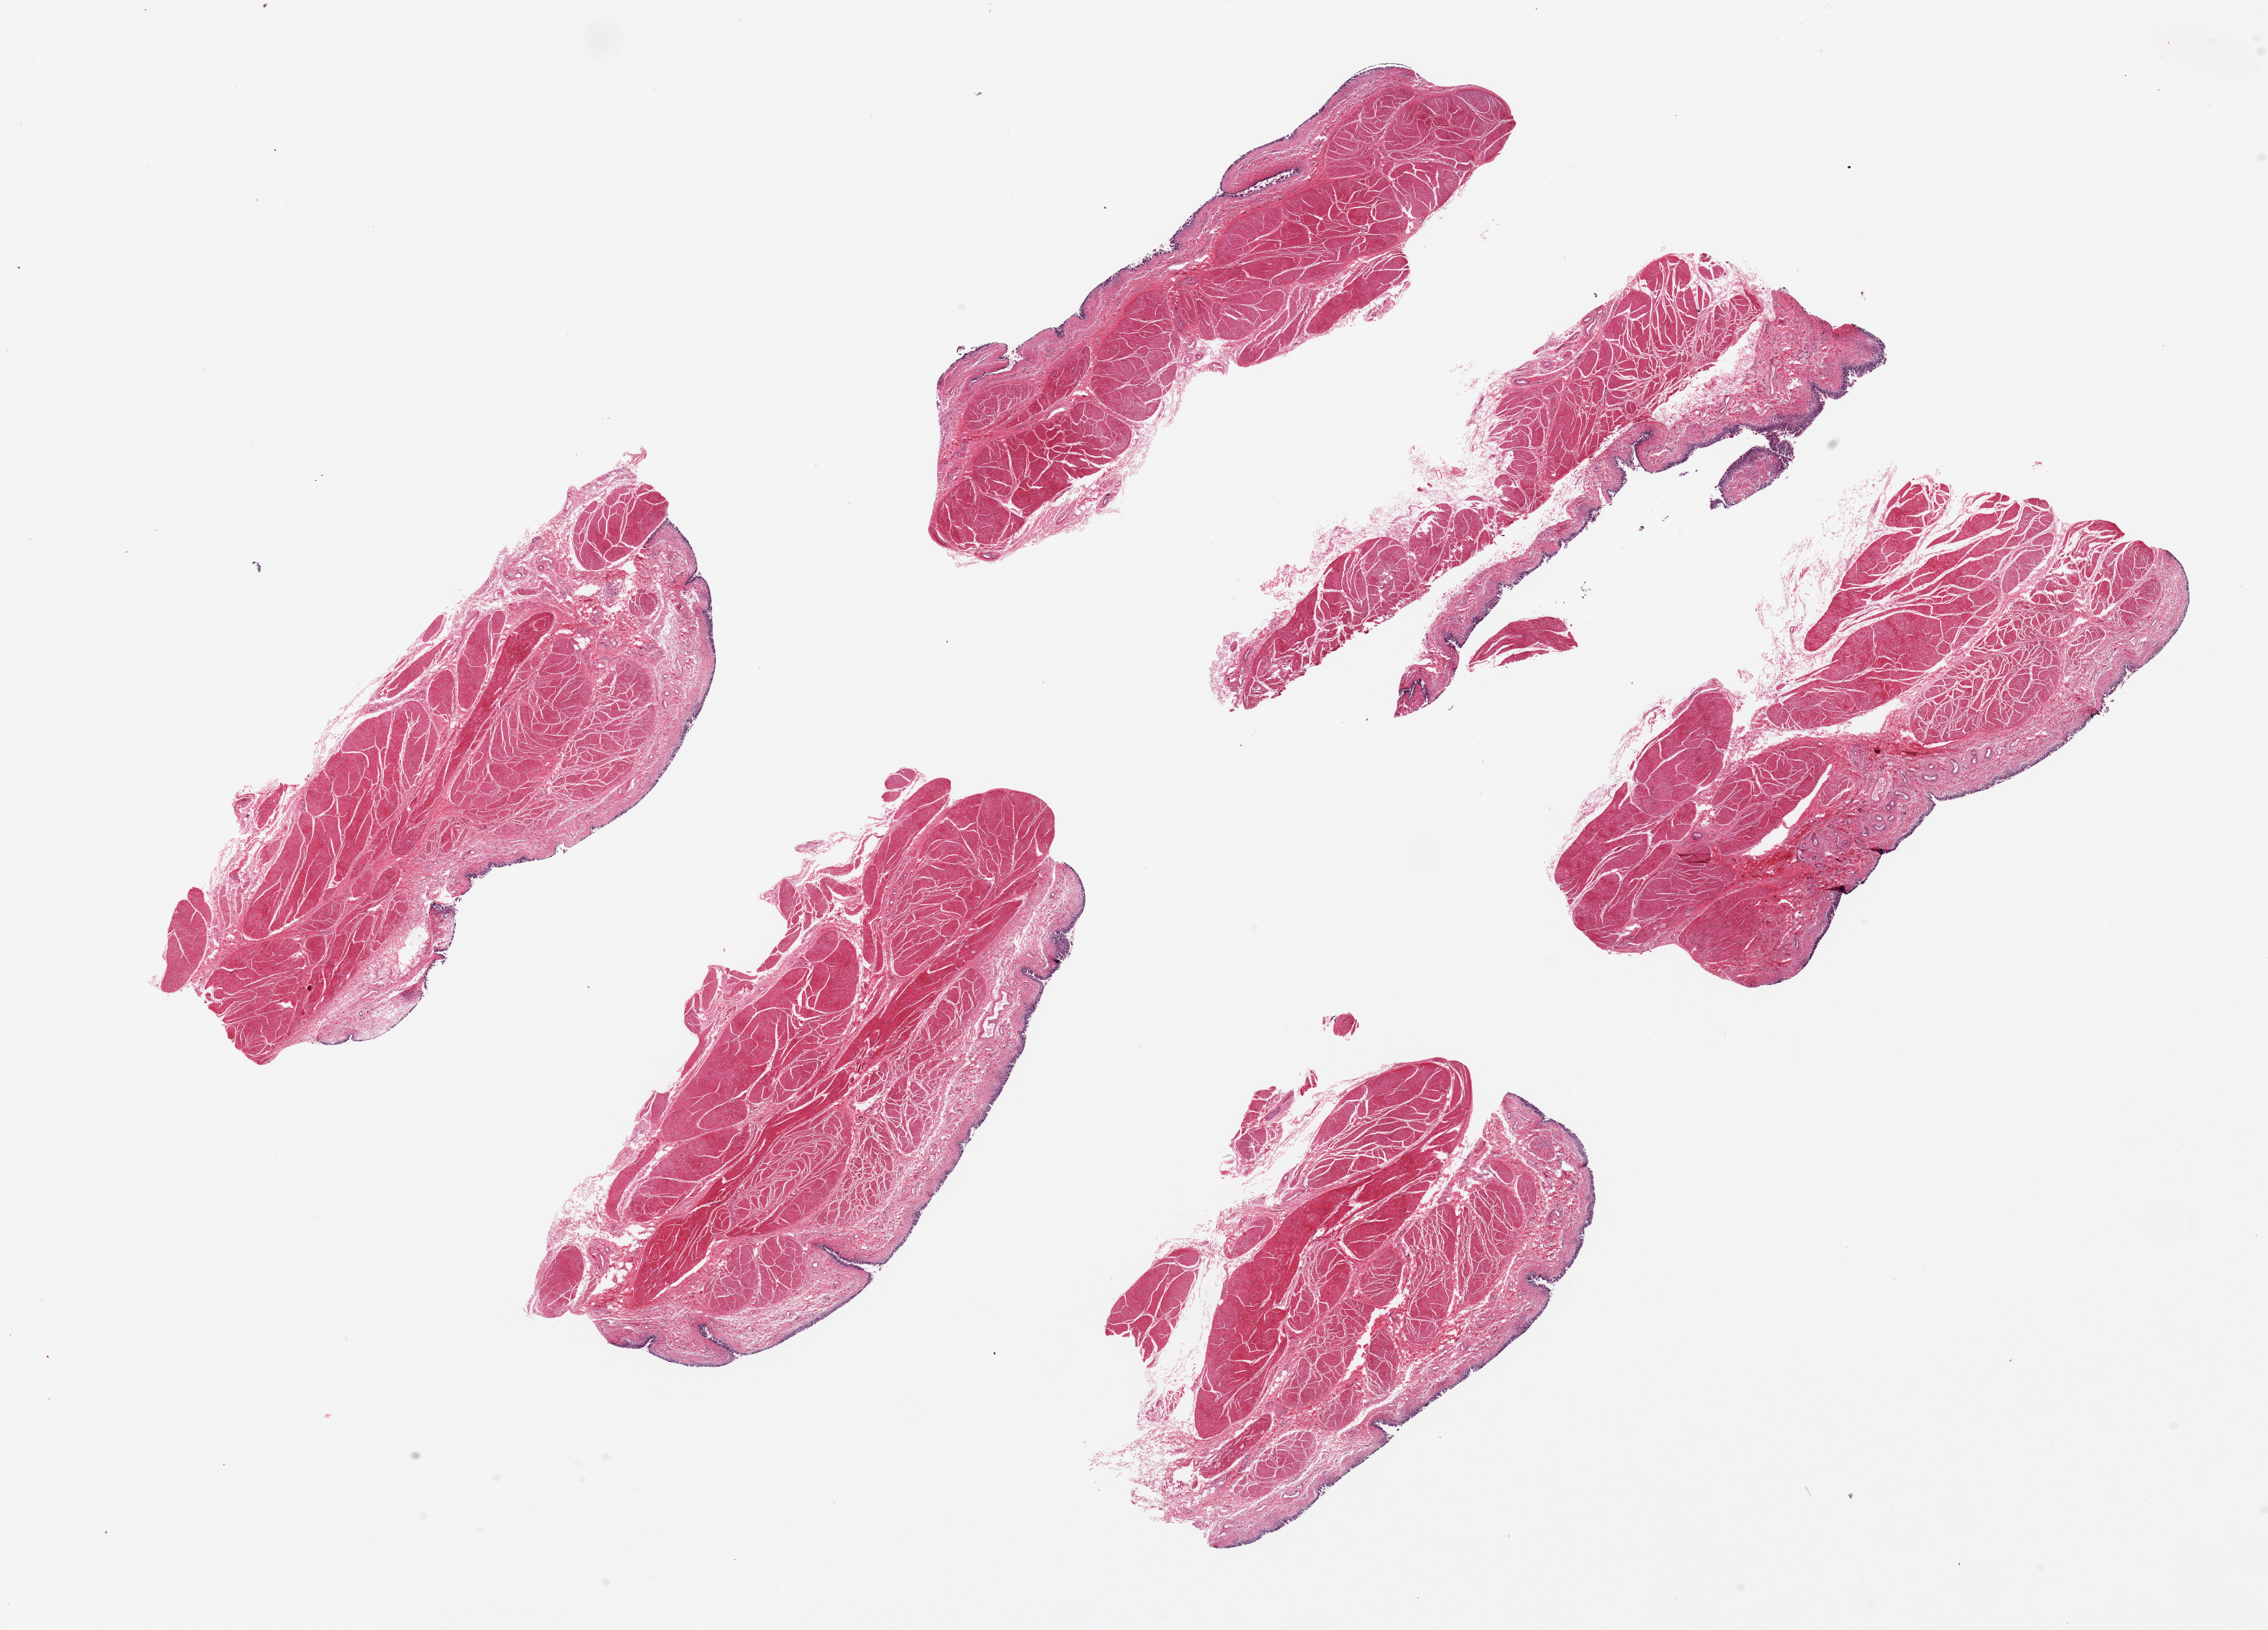
Digitized hematoxylin and eosin (H&E)-stained section, brightfield — low-resolution overview of the scanned area, about 27.6 x 19.8 mm (slide scanned at 20x). PAXgene-fixed, paraffin-embedded tissue. Target tissue: urinary bladder. Donor tissue sample. Male donor.
Reviewer comment on this tissue sample: 6 pieces, ~5 x 7mm, mucosa partly sloughed.